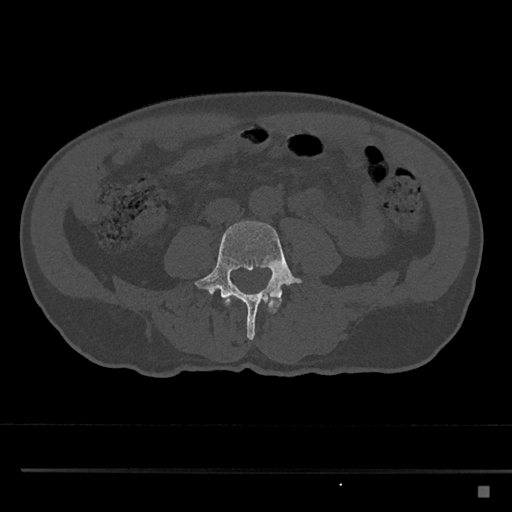
CT including the spine, one axial slice. Slice 640 of 797 in the series (ordered by position). 120 kVp. Bone window (W 1800 / L 400 HU). 0.5 mm slice thickness. 512 × 512 image matrix, field of view 391 × 391 mm. Male patient, age 59 years. Case-level facts recorded for this patient, not image findings: primary cancer: prostate.
Annotated regions visible in this slice (semi-automatic segmentation, software-assisted and operator-edited):
- L3 vertebra: bounding box [x1, y1, x2, y2] px = [224, 297, 280, 313]
- L4 vertebra: [194, 221, 302, 340]
- L5 vertebra: [206, 289, 211, 295]